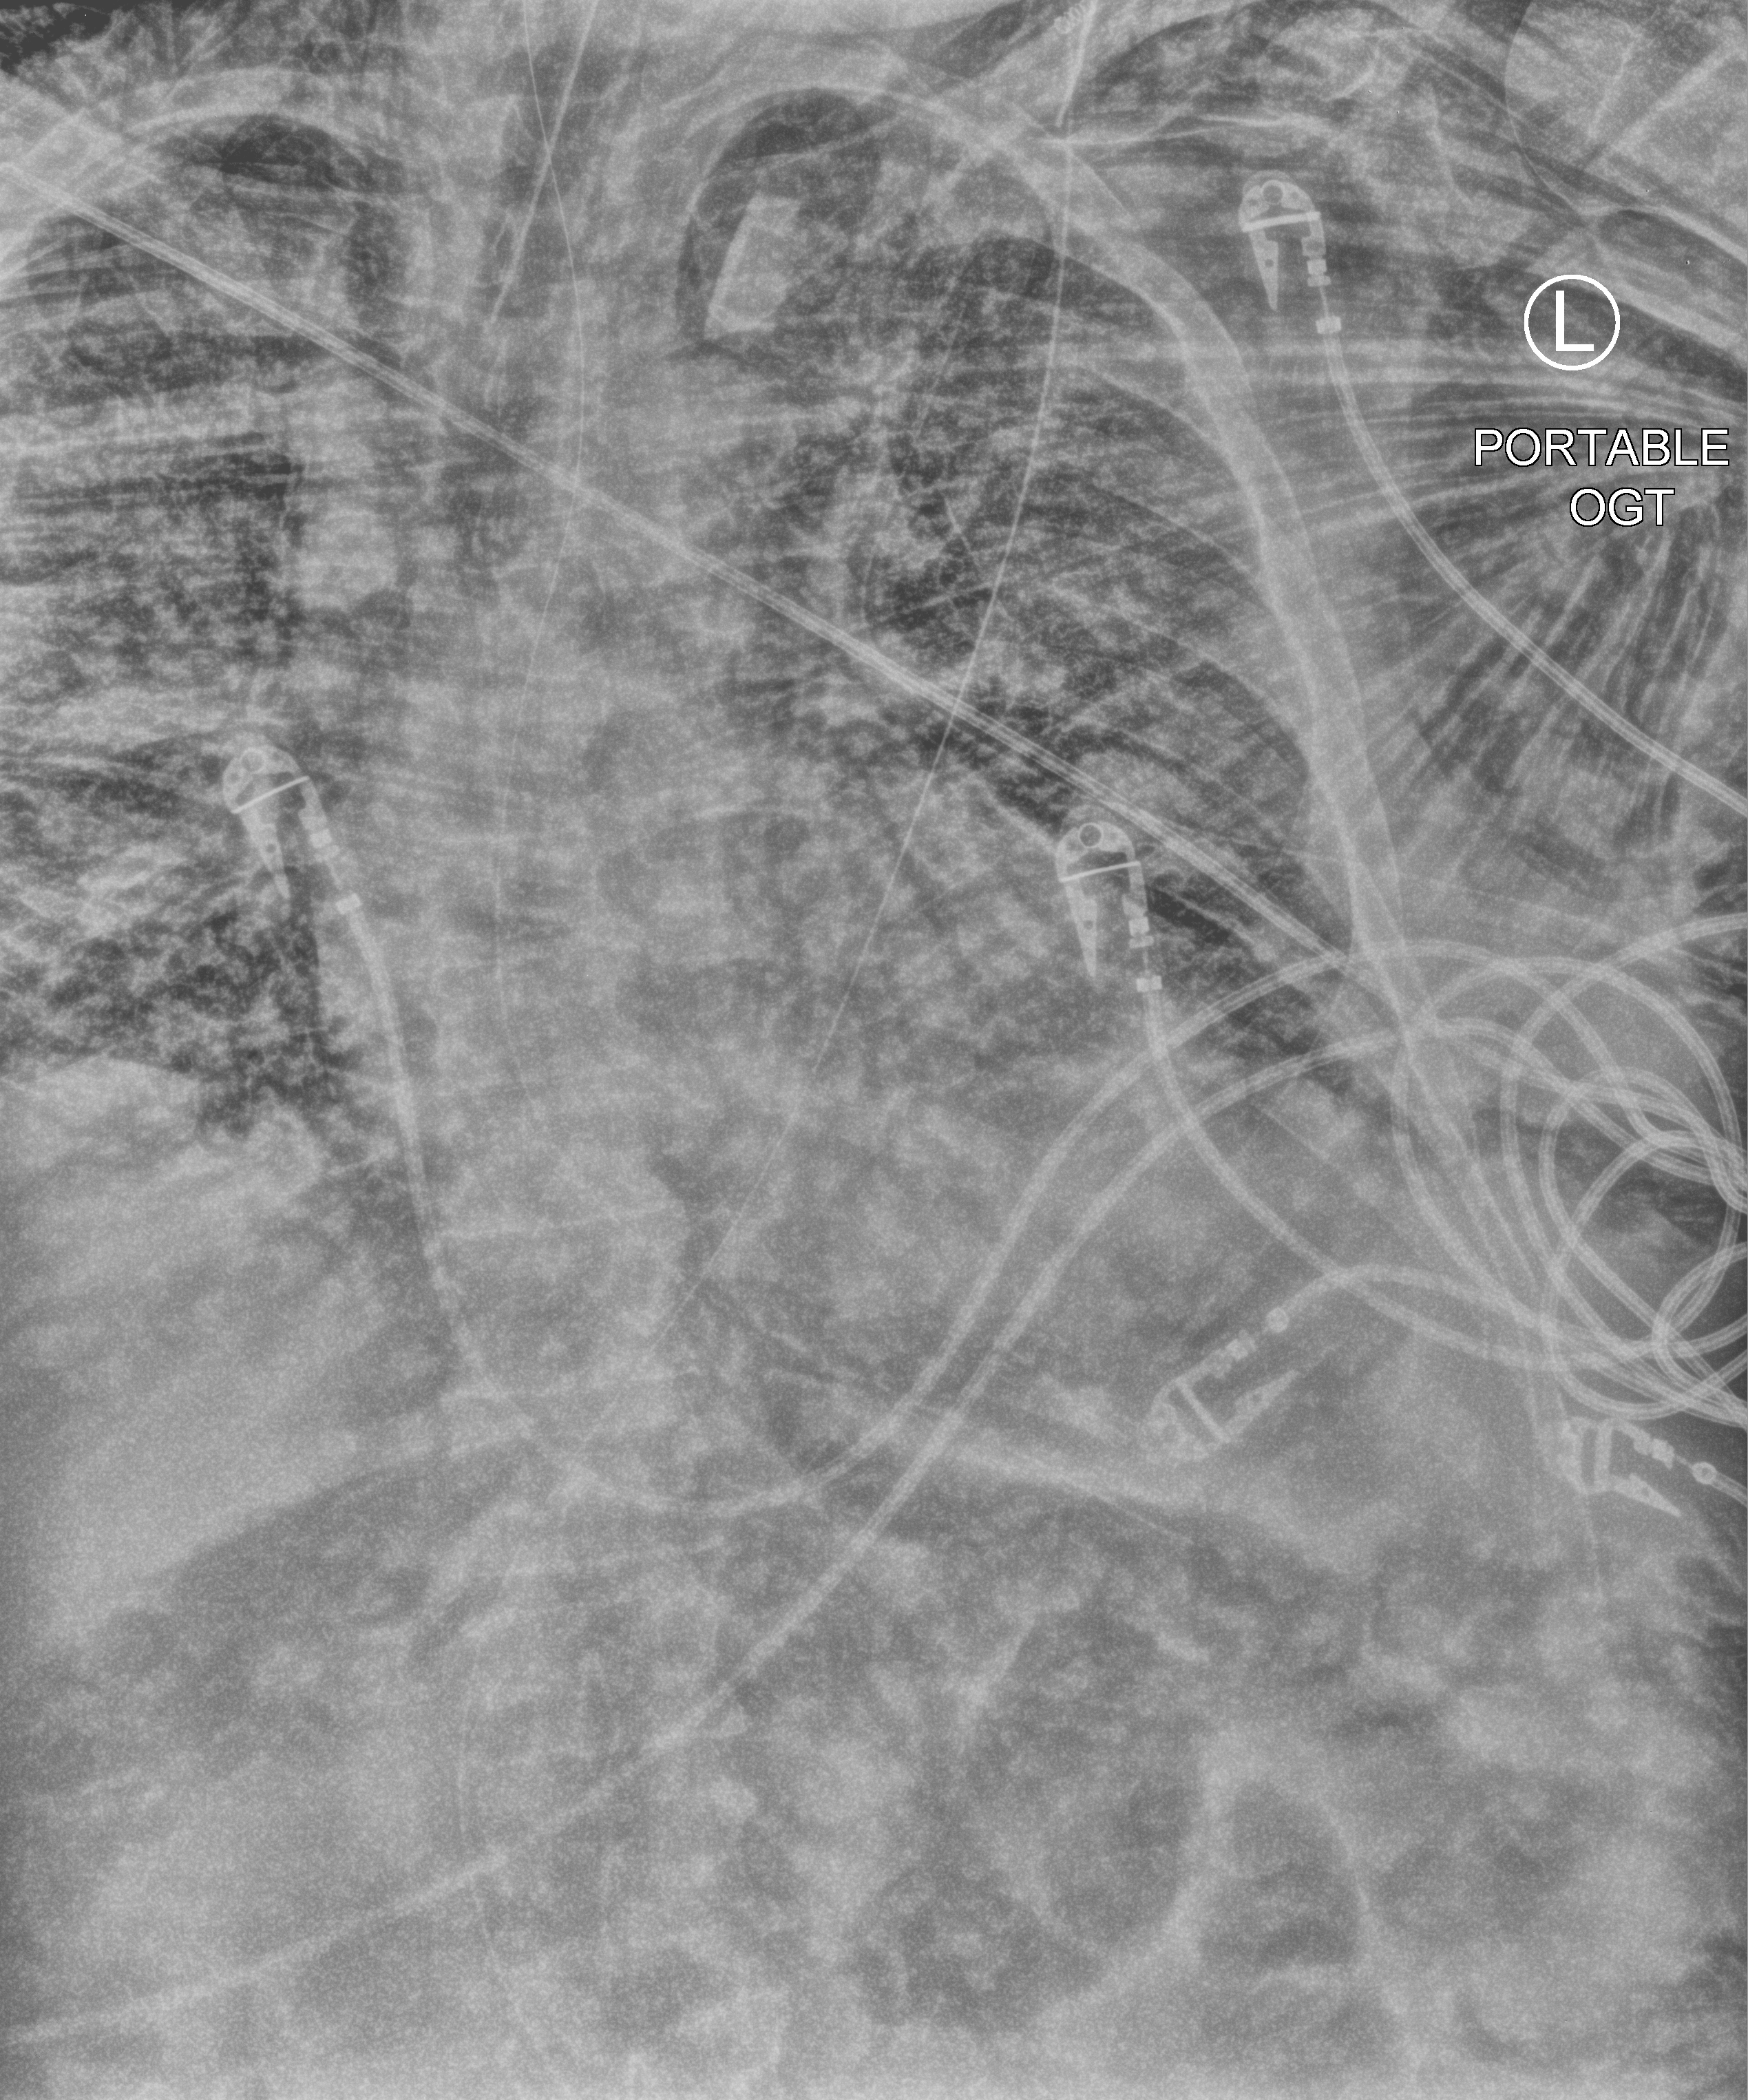
Chest X-ray (portable); anteroposterior (AP) projection. Patient hospitalised with COVID-19, aged 18–59 years.
Hospital-stay facts (about this admission, not read from this image; timing relative to this image not recorded):
- mechanically ventilated during this hospital stay: yes